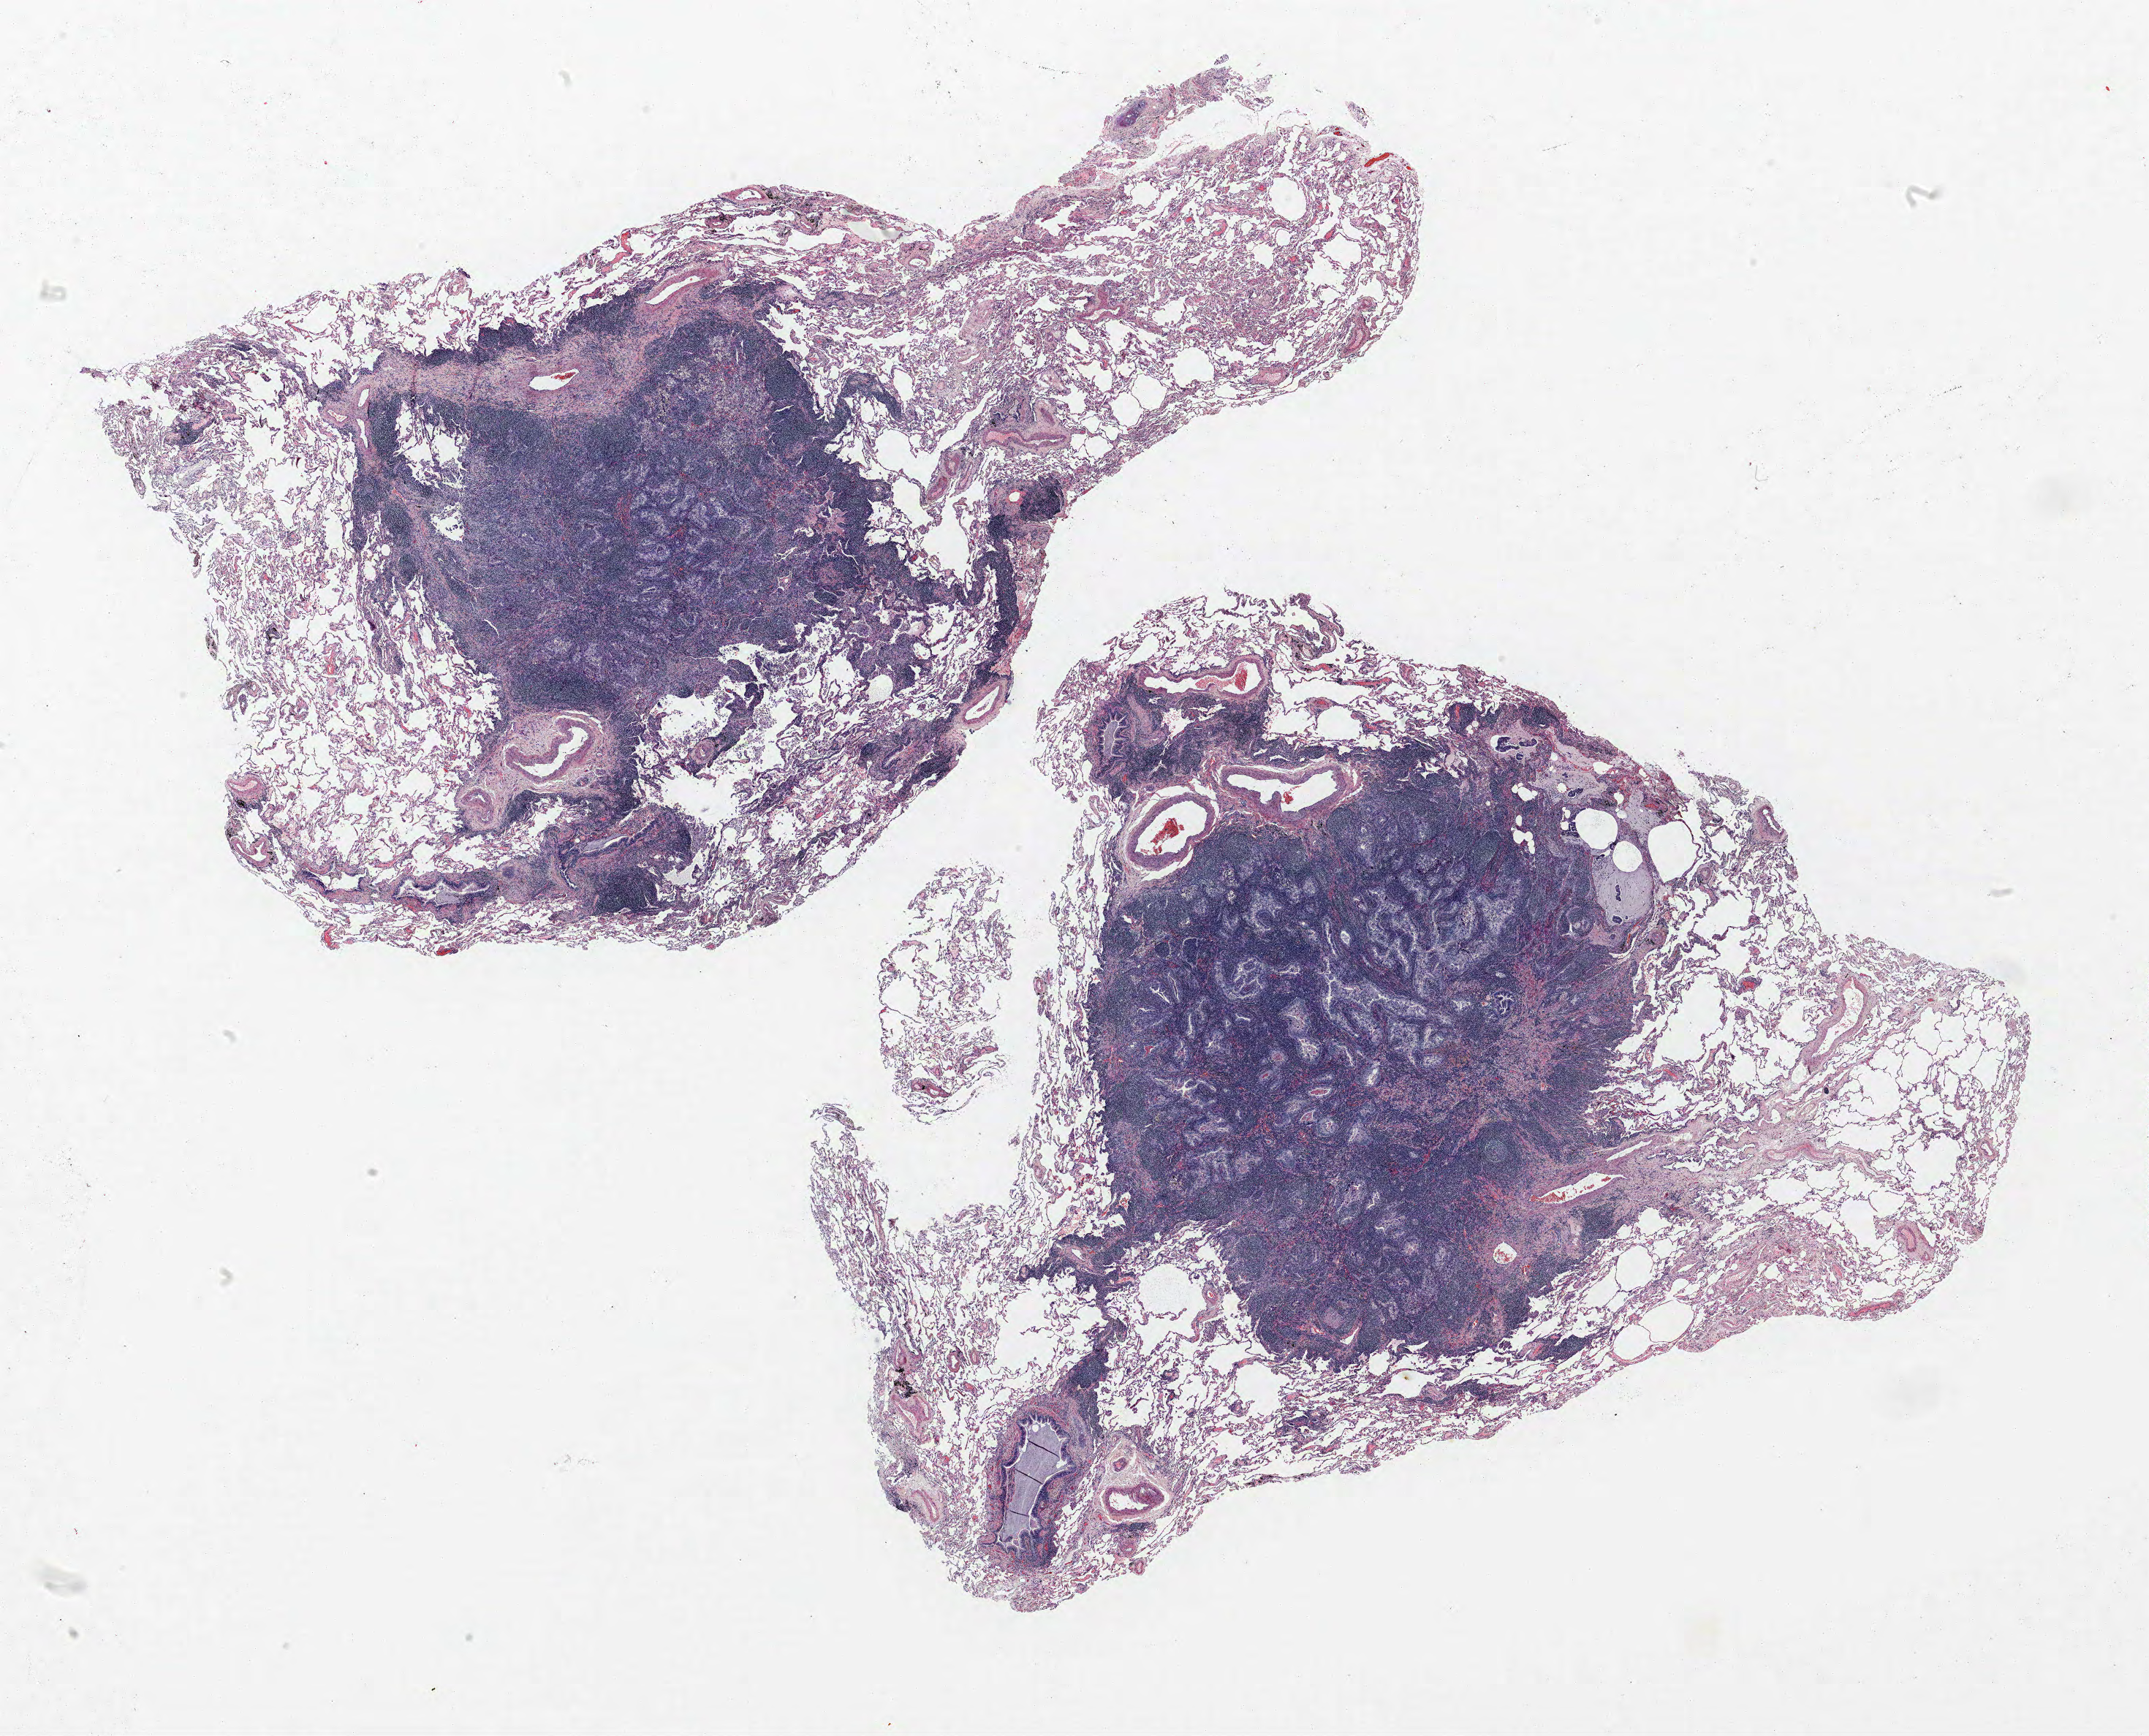
Hematoxylin and eosin (H&E) stained whole-slide image, whole scanned area (about 23.5 x 19.0 mm) shown as a low-resolution overview; formalin-fixed paraffin-embedded (FFPE) section; lung tissue. Female patient, aged 64 at enrolment. Current smoker at enrolment. Grade: moderately differentiated (G2).
Participant's lung-cancer diagnosis: Adenocarcinoma, NOS. Stage (AJCC 6th edition): IA. Primary tumour location (clinical record): left upper lobe. Tumour size (pathology): 7 mm.